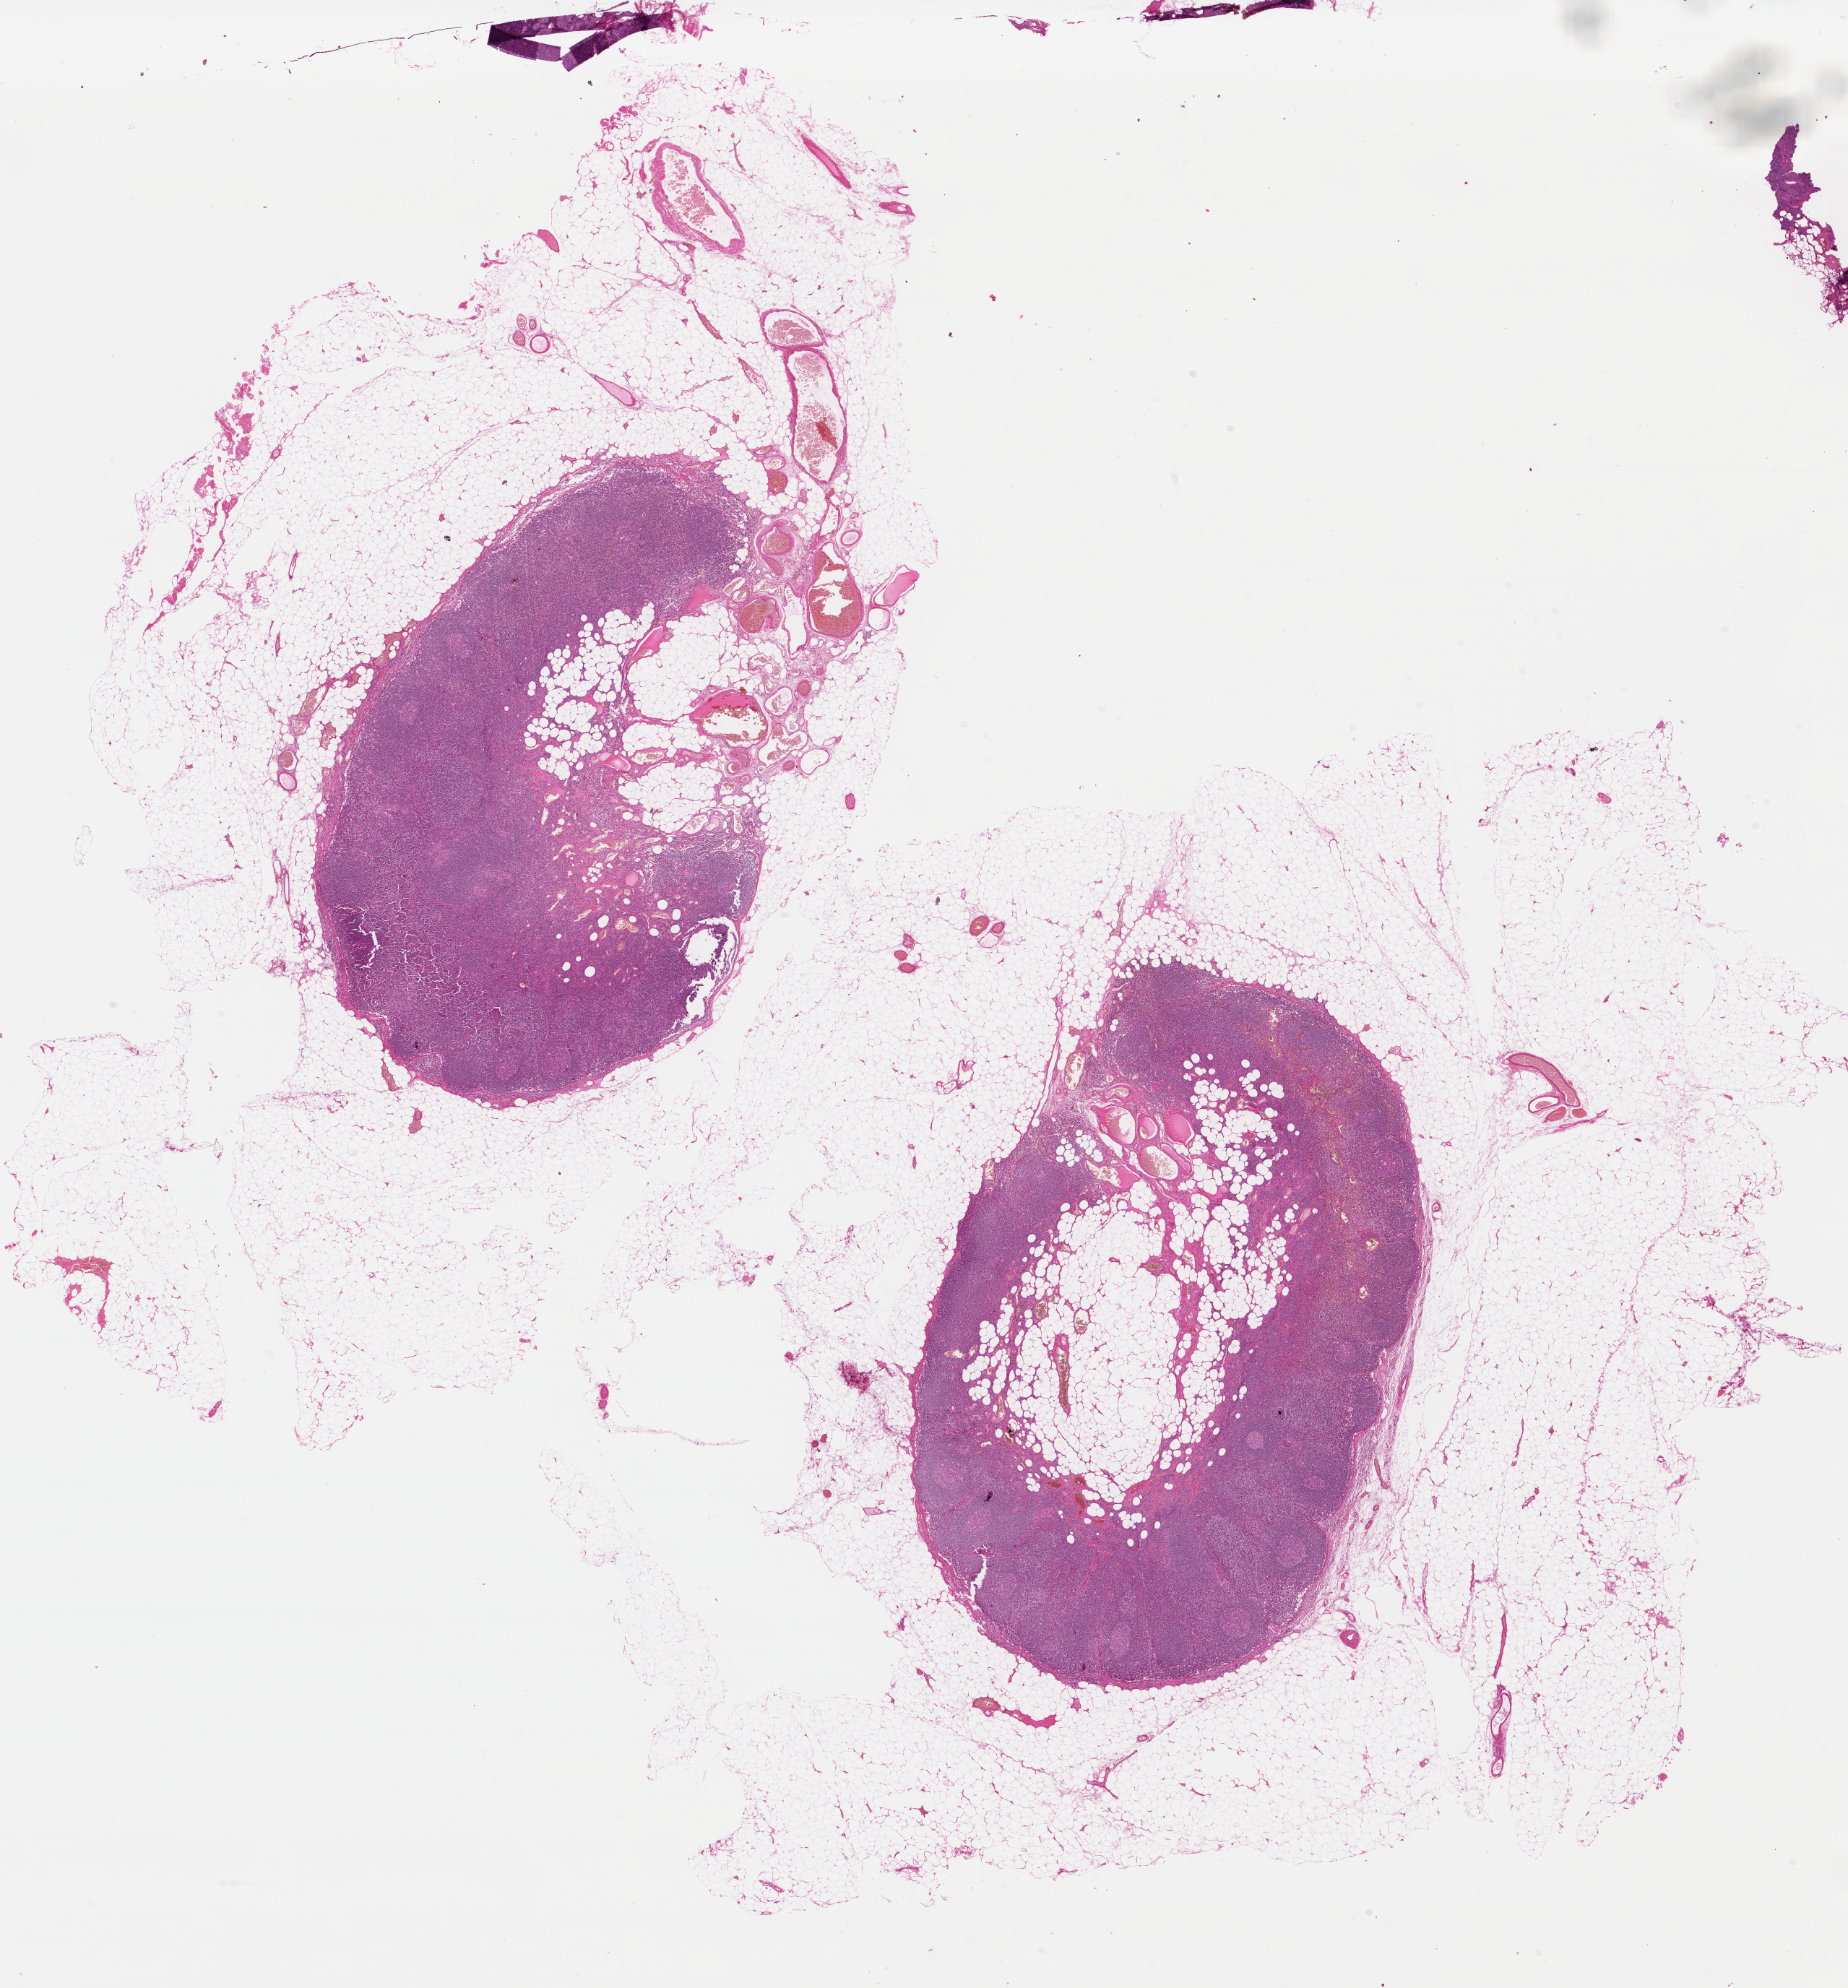
Whole-slide histology image, H&E-stained — whole scanned area (about 20.1 x 21.6 mm, acquisition: 40x scan) shown as a low-resolution overview. Formalin-fixed paraffin-embedded (FFPE) diagnostic section. Primary tumour sample from the skin. Patient: female, age at initial diagnosis 34 years.
* histologic diagnosis: Malignant melanoma, NOS